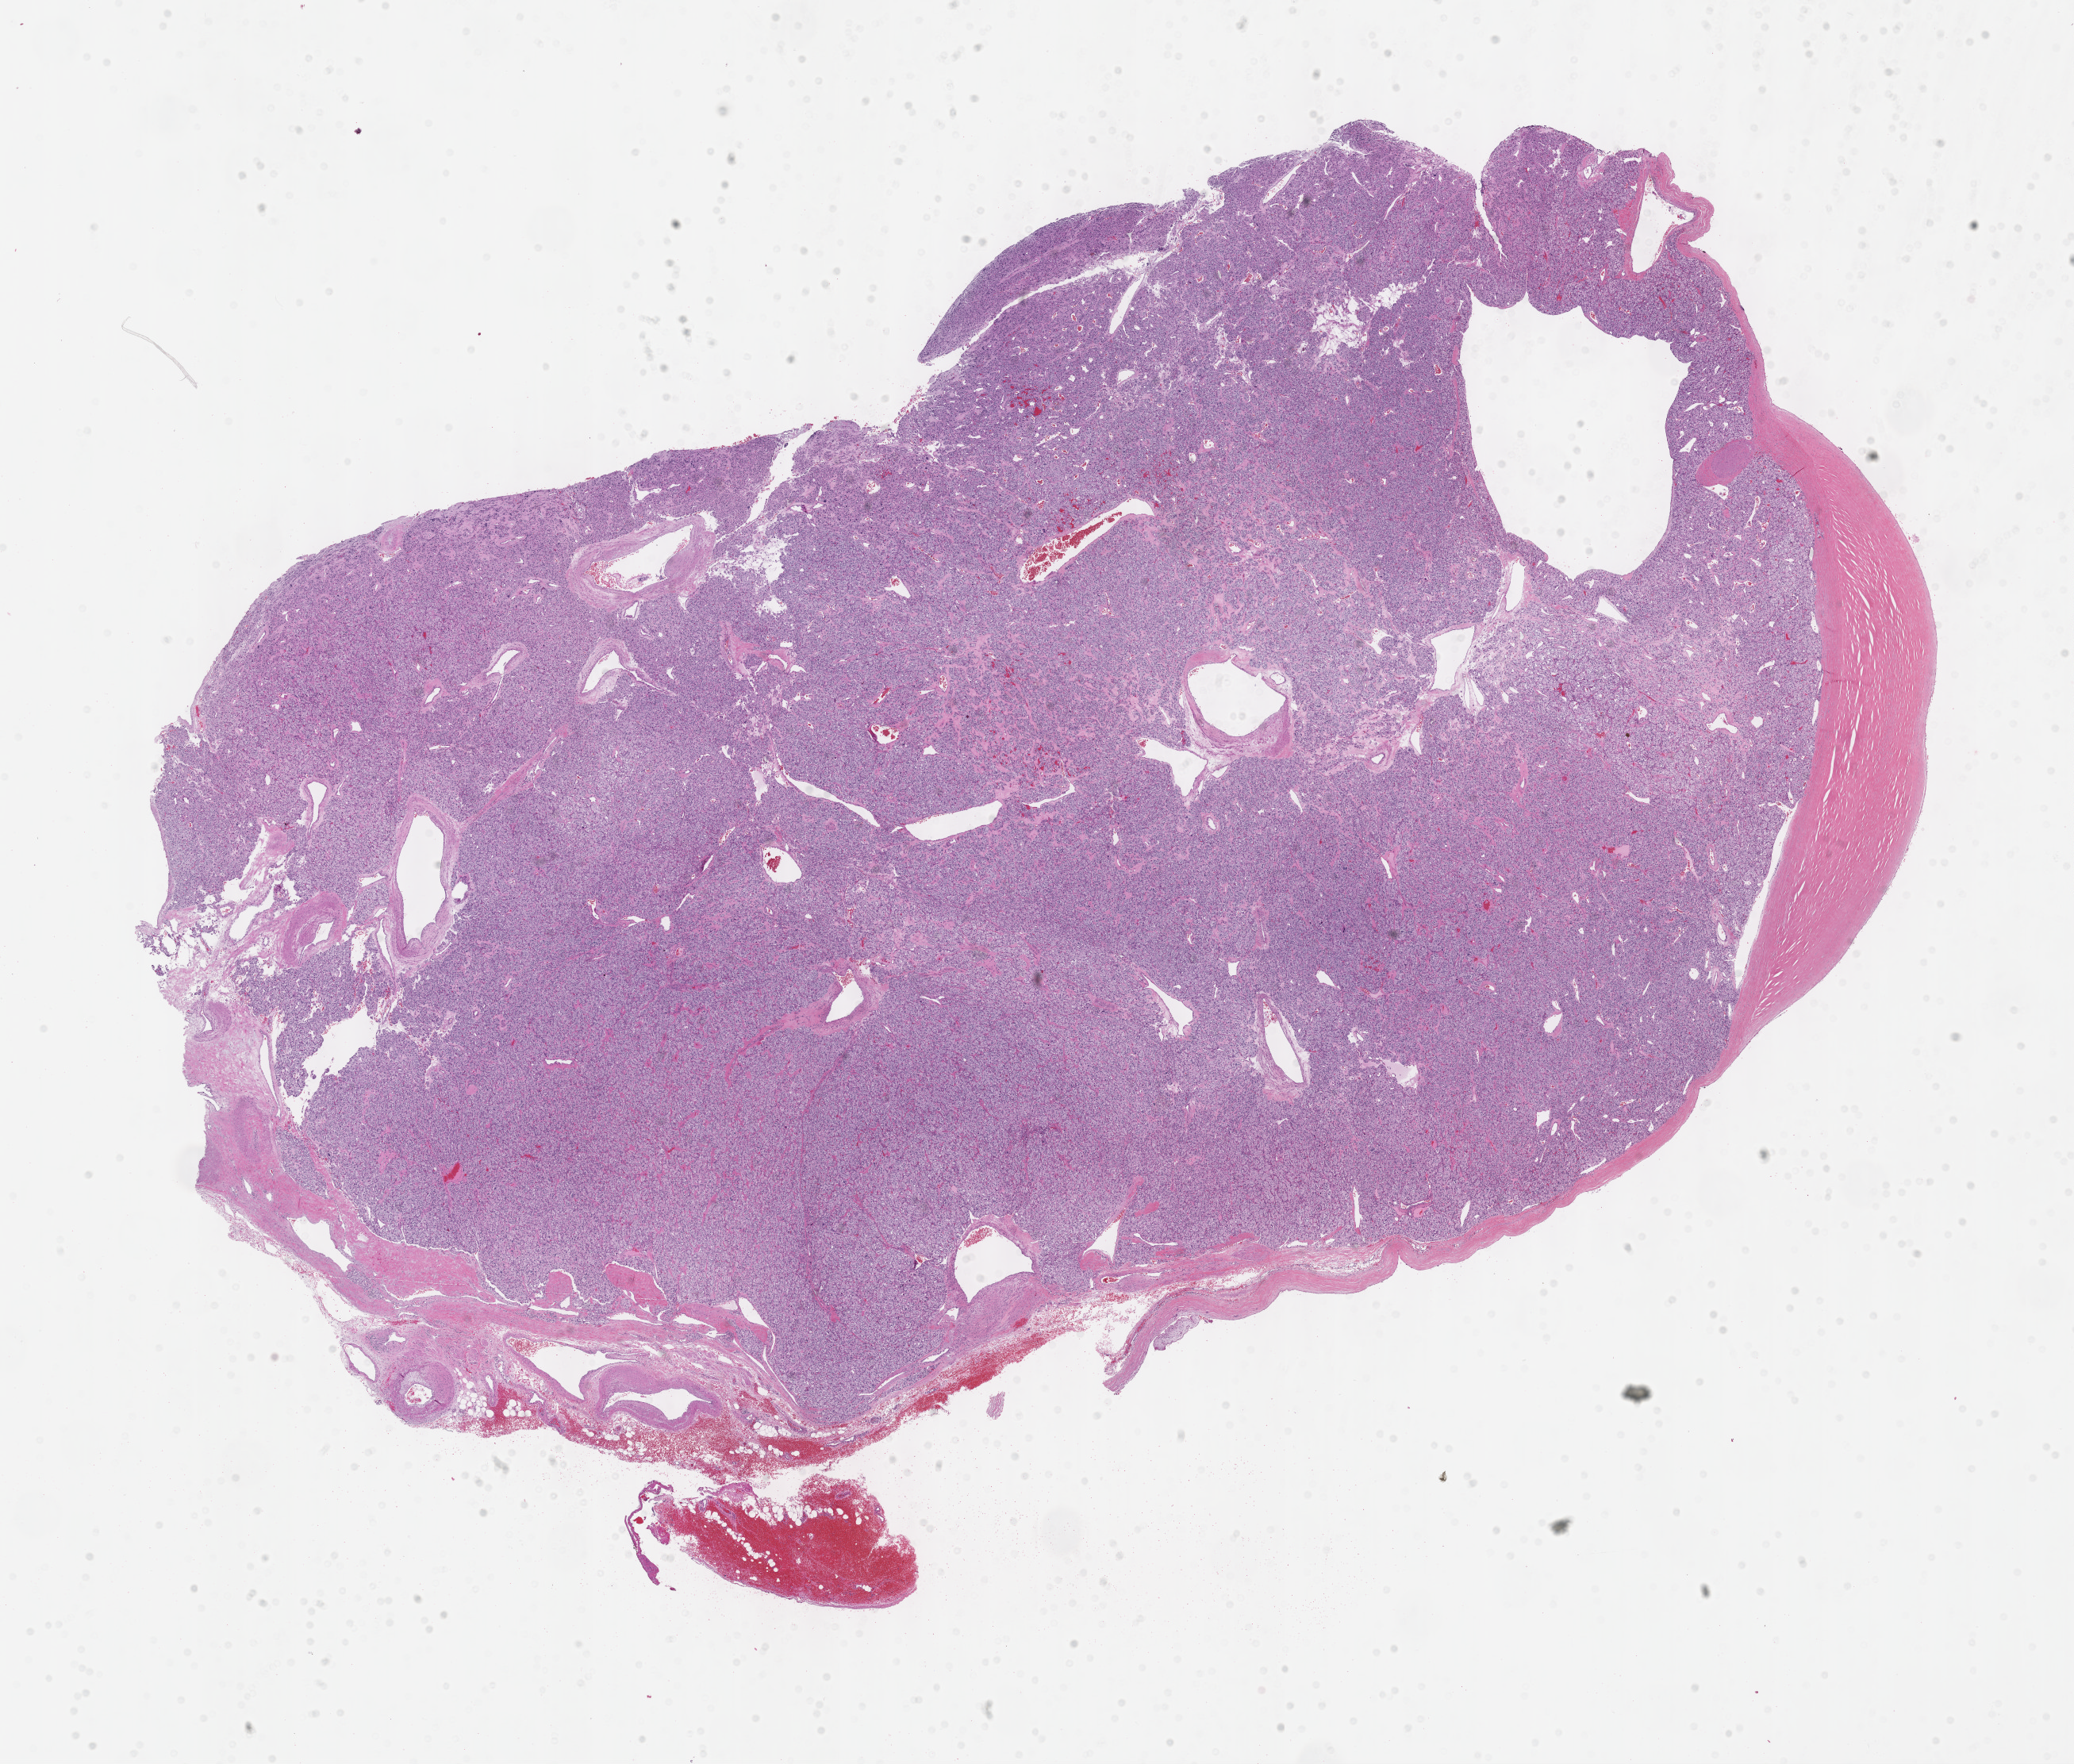
Whole-slide histology image, H&E — whole scanned area (about 21.1 x 18.0 mm, slide scanned at 40x) shown as a low-resolution overview. Formalin-fixed paraffin-embedded (FFPE) diagnostic section. Primary tumour sample. Male, age 41 years at initial diagnosis.
Pathologic diagnosis: Extra-adrenal paraganglioma, NOS (thorax, NOS).